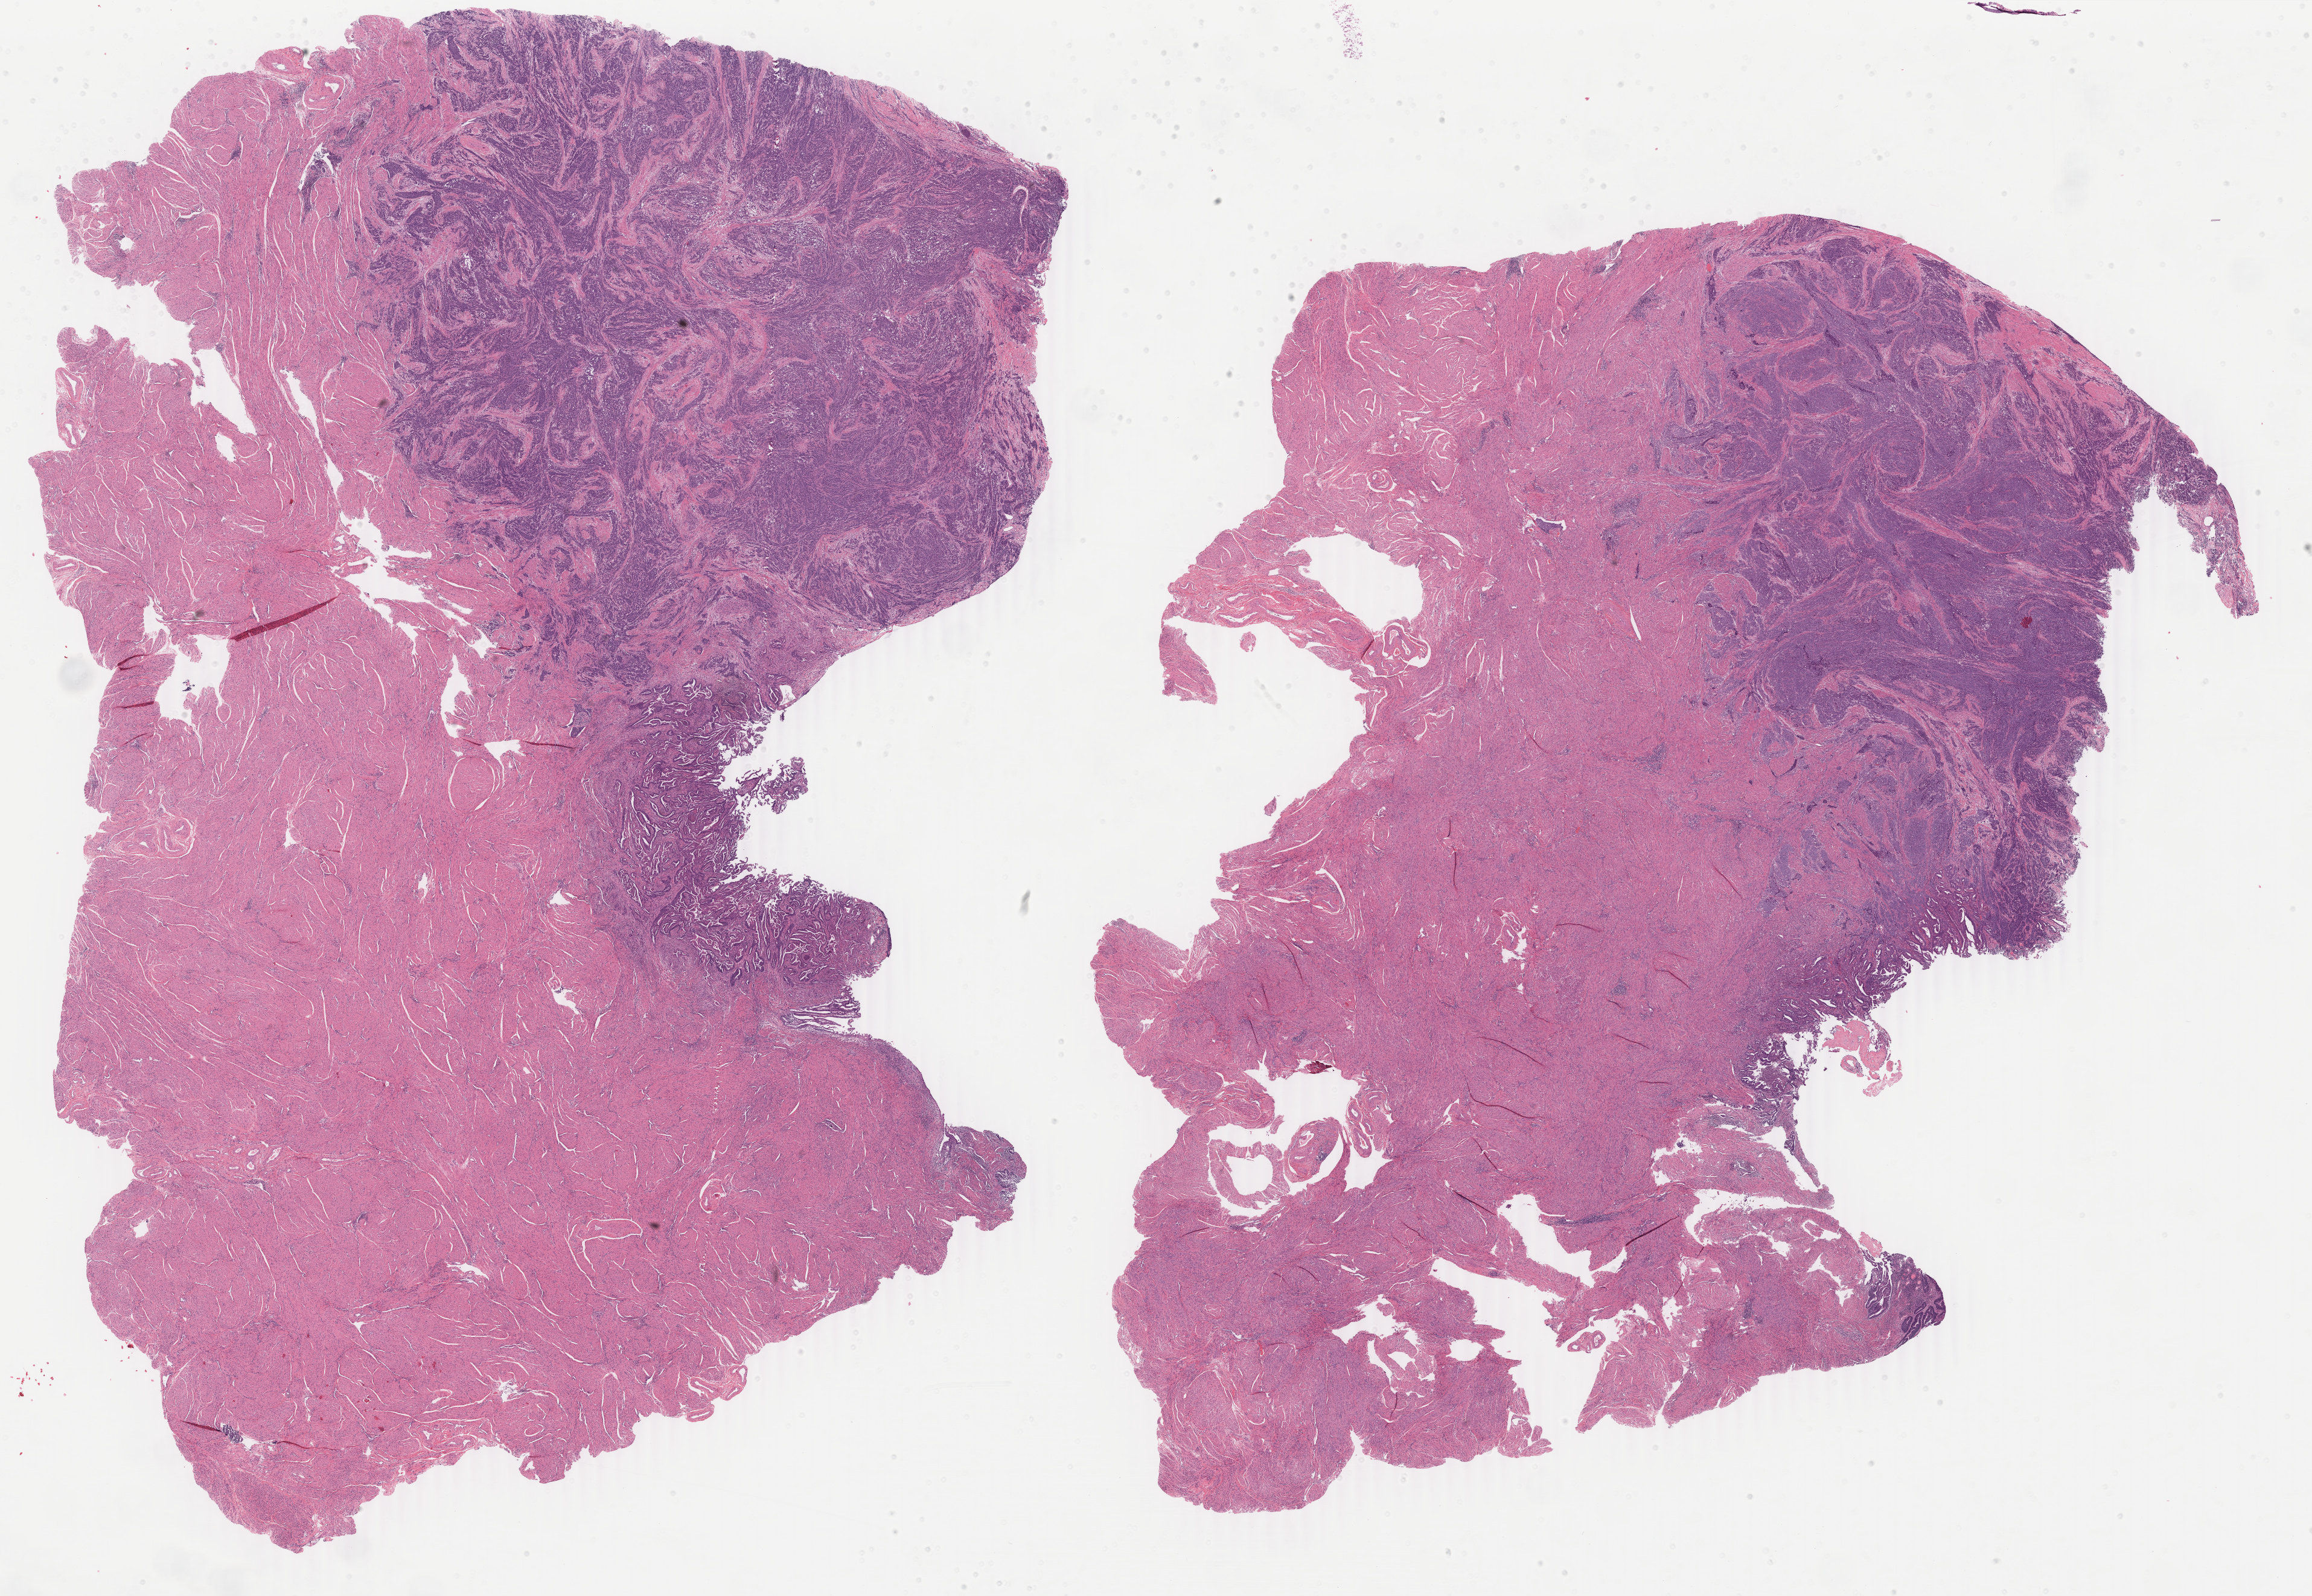
Whole-slide histology image, H&E, a low-resolution overview of the entire scanned area, about 30.5 x 21.0 mm (from a 40x scan). Formalin-fixed paraffin-embedded (FFPE) diagnostic section. Primary tumour sample from the uterus. Female patient; age at initial diagnosis 54 years. Histologic grade: G3 (poorly differentiated).
Histologic diagnosis: Endometrioid adenocarcinoma, NOS (endometrium). FIGO stage: IB.